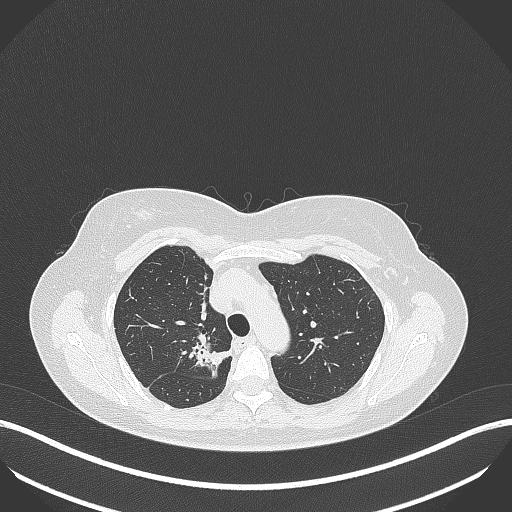
Chest CT, one axial slice; position 292 of 386 along the scan axis; 120 kVp; lung window (W 1500 / L -600 HU); 1 mm slice thickness; 512 × 512 image matrix, field of view 400 × 400 mm. Patient: female, 65 years. From the clinical record (not read from this slice): clinical TNM (as recorded): T1b N0 M0; histopathological grade: G2.
Annotated regions visible in this slice (bounding box drawn by a radiologist):
- lung tumour (recorded histology: adenocarcinoma): bounding box (x1, y1, x2, y2) in pixels: (187, 338, 234, 382)